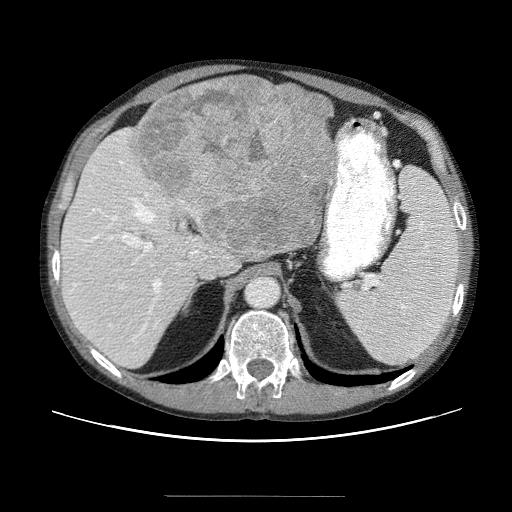
Contrast-enhanced abdominal CT (liver protocol), one axial slice. Slice 34 of 69 in the series (ordered by position). 120 kVp. Soft-tissue window (W 400 / L 40 HU). 2.5 mm slice thickness. 512 × 512 image matrix, field of view 380 × 380 mm. From the clinical record (not read from this slice): diagnosis: hepatocellular carcinoma (patient treated with transarterial chemoembolisation; whether this scan precedes or follows treatment is not stated here); TNM stage (as recorded): Stage-IVB; Child-Pugh class: B; tumour differentiation: poorly differentiated.
Outlined on this slice (semi-automatic segmentation, software-assisted and operator-edited):
- abdominal aorta: bounding box [x1, y1, x2, y2] px = [245, 277, 278, 307]
- liver parenchyma outside the tumour (the mass and vessels are separate outlines, so this box may not span the whole liver): [60, 84, 330, 368]
- mass: [132, 75, 336, 257]
- liver vessels: [71, 159, 215, 351]